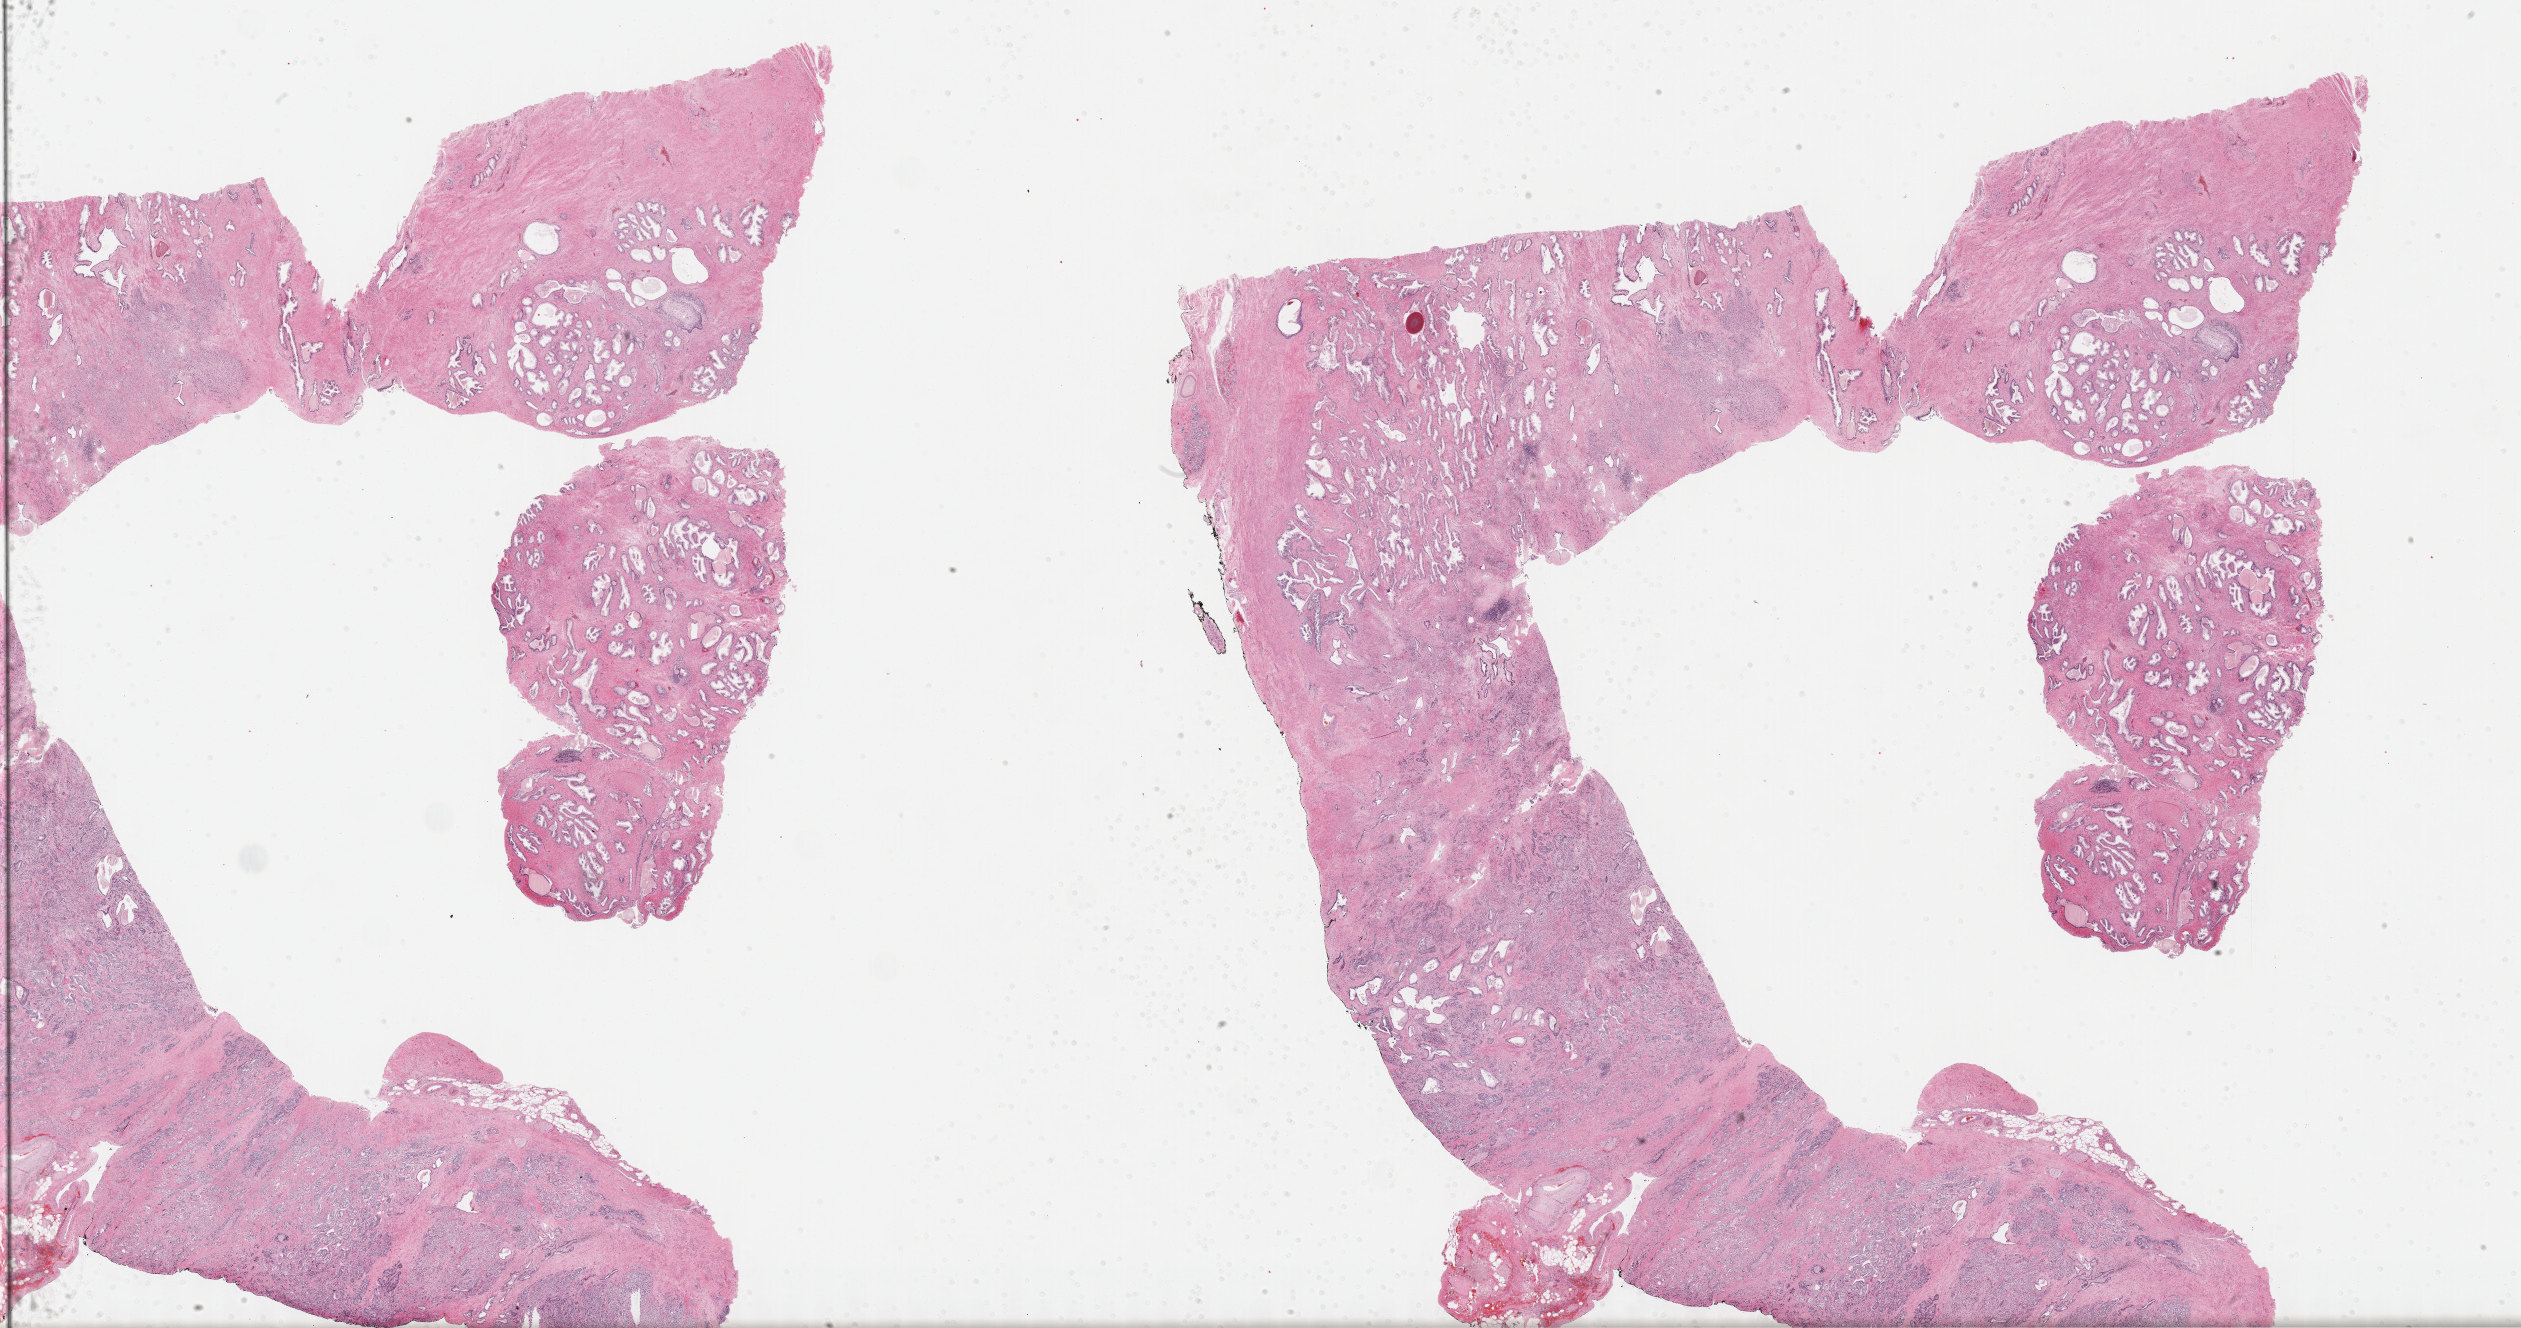
H&E-stained whole-slide image, low-resolution overview of the scanned area, about 40.8 x 21.5 mm. Formalin-fixed paraffin-embedded (FFPE) diagnostic section. Primary tumour sample from the prostate. Male patient; age at initial diagnosis 65 years. Gleason score: 9 (4+5).
* lymph nodes positive (case pathology): 0 of 3 examined
* diagnosis: Adenocarcinoma, NOS (prostate gland)